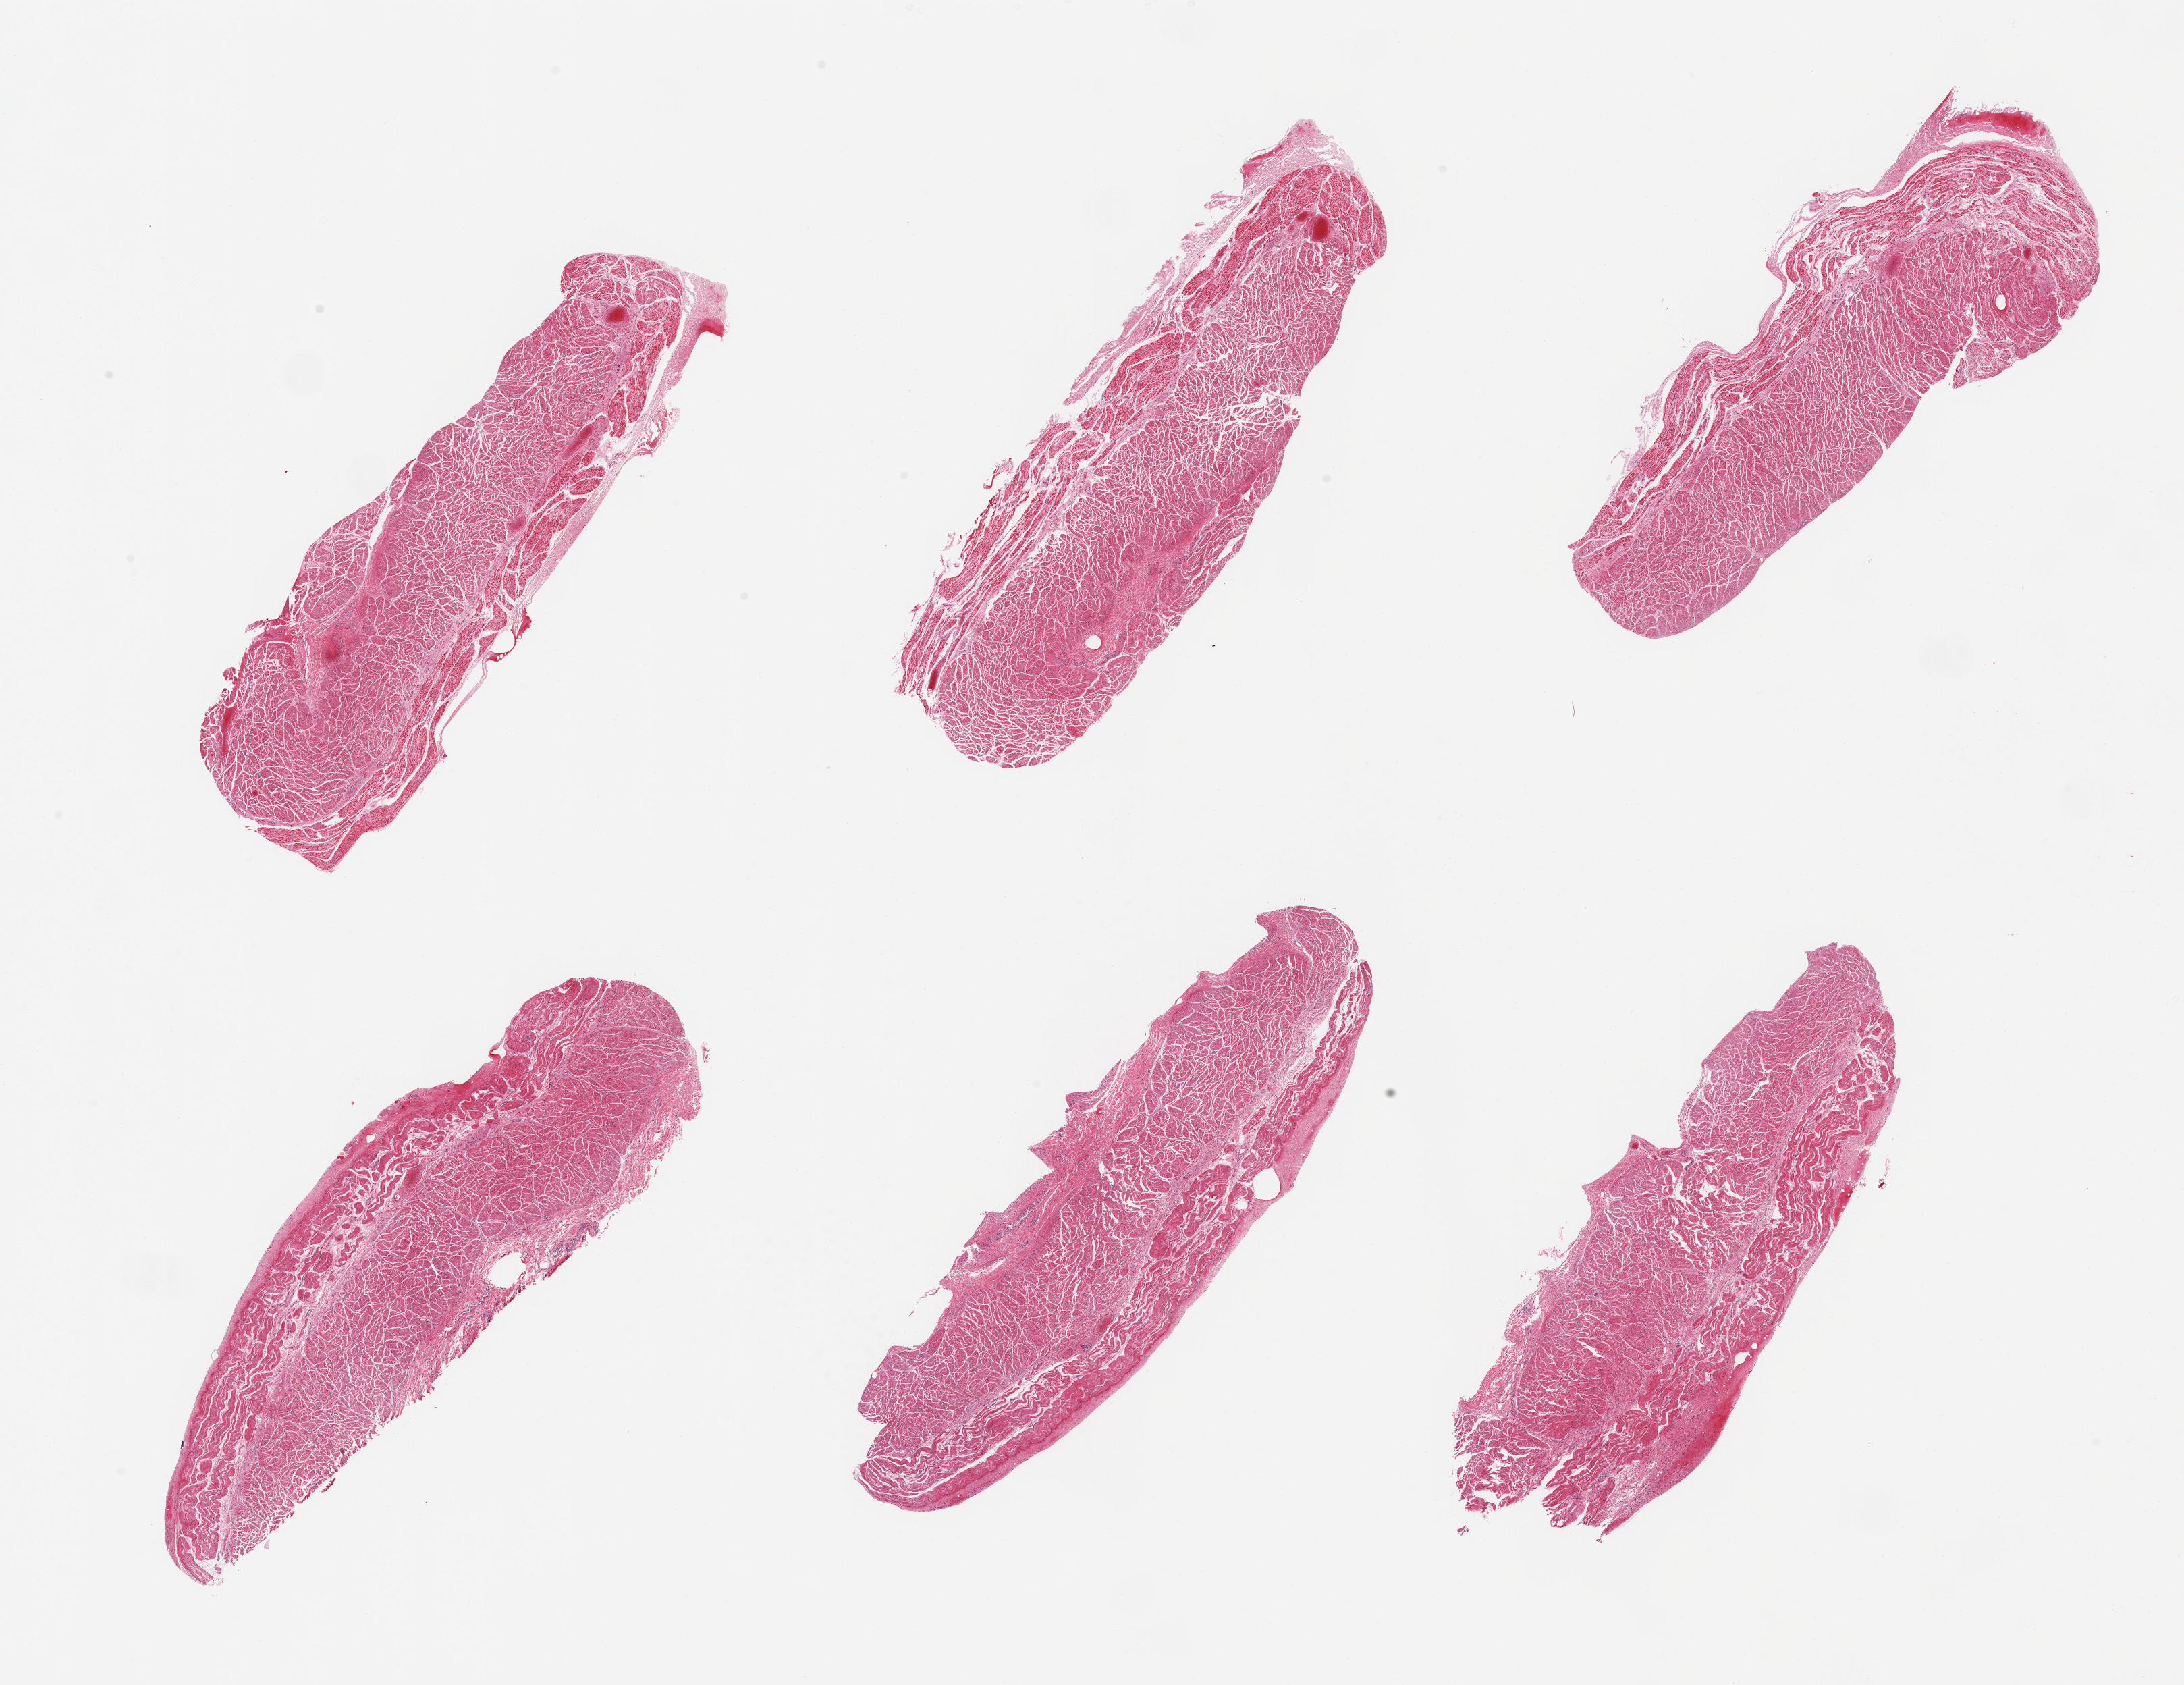
Whole-slide image, hematoxylin and eosin (H&E) stain, shown as a low-resolution overview of the whole scanned area (about 25.6 x 19.7 mm, slide scanned at 20x), PAXgene-fixed, paraffin-embedded tissue, sampled site (target tissue): esophageal muscle, tissue donor sample. Donor sex: male.
• review note (as recorded): 6 pieces; well trimmed target muscularis